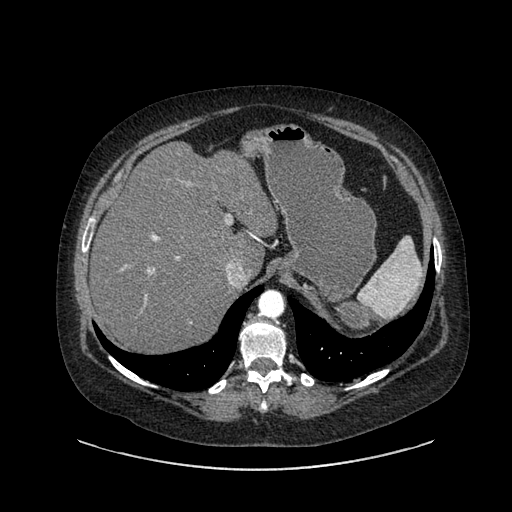
Contrast-enhanced abdominal CT, one axial slice. Slice 641 of 769 in the series (ordered by position). 120 kVp. Intravenous contrast given. Soft-tissue window (W 400 / L 40 HU). 512 × 512 image matrix, field of view 460 × 460 mm. Female patient, age 61 years. Case-level facts recorded for this patient, not image findings: diagnosis: adrenocortical carcinoma; tumour side: left adrenal; tumour size at pathology: 13 cm; Ki-67 index: 79 %.
Structures marked on this image (semi-automatically segmented with operator editing):
- mass: bounding box <331,301,372,337> (left, top, right, bottom; pixels)